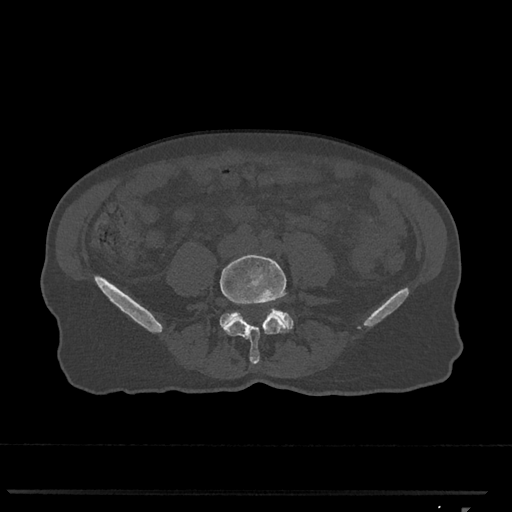
CT including the spine, one axial slice. Position 189 of 793 along the scan axis. Reconstruction kernel Br40s/3. Bone window (W 1800 / L 400 HU). 512 × 512 image matrix, field of view 380 × 380 mm. Female patient, age 62 years. Case-level facts recorded for this patient, not image findings: primary cancer: renal.
Structures marked on this image (semi-automatic segmentation, software-assisted and operator-edited):
- L4 vertebra: bounding box [x1, y1, x2, y2] px = [220, 255, 289, 364]
- L5 vertebra: [219, 308, 294, 330]